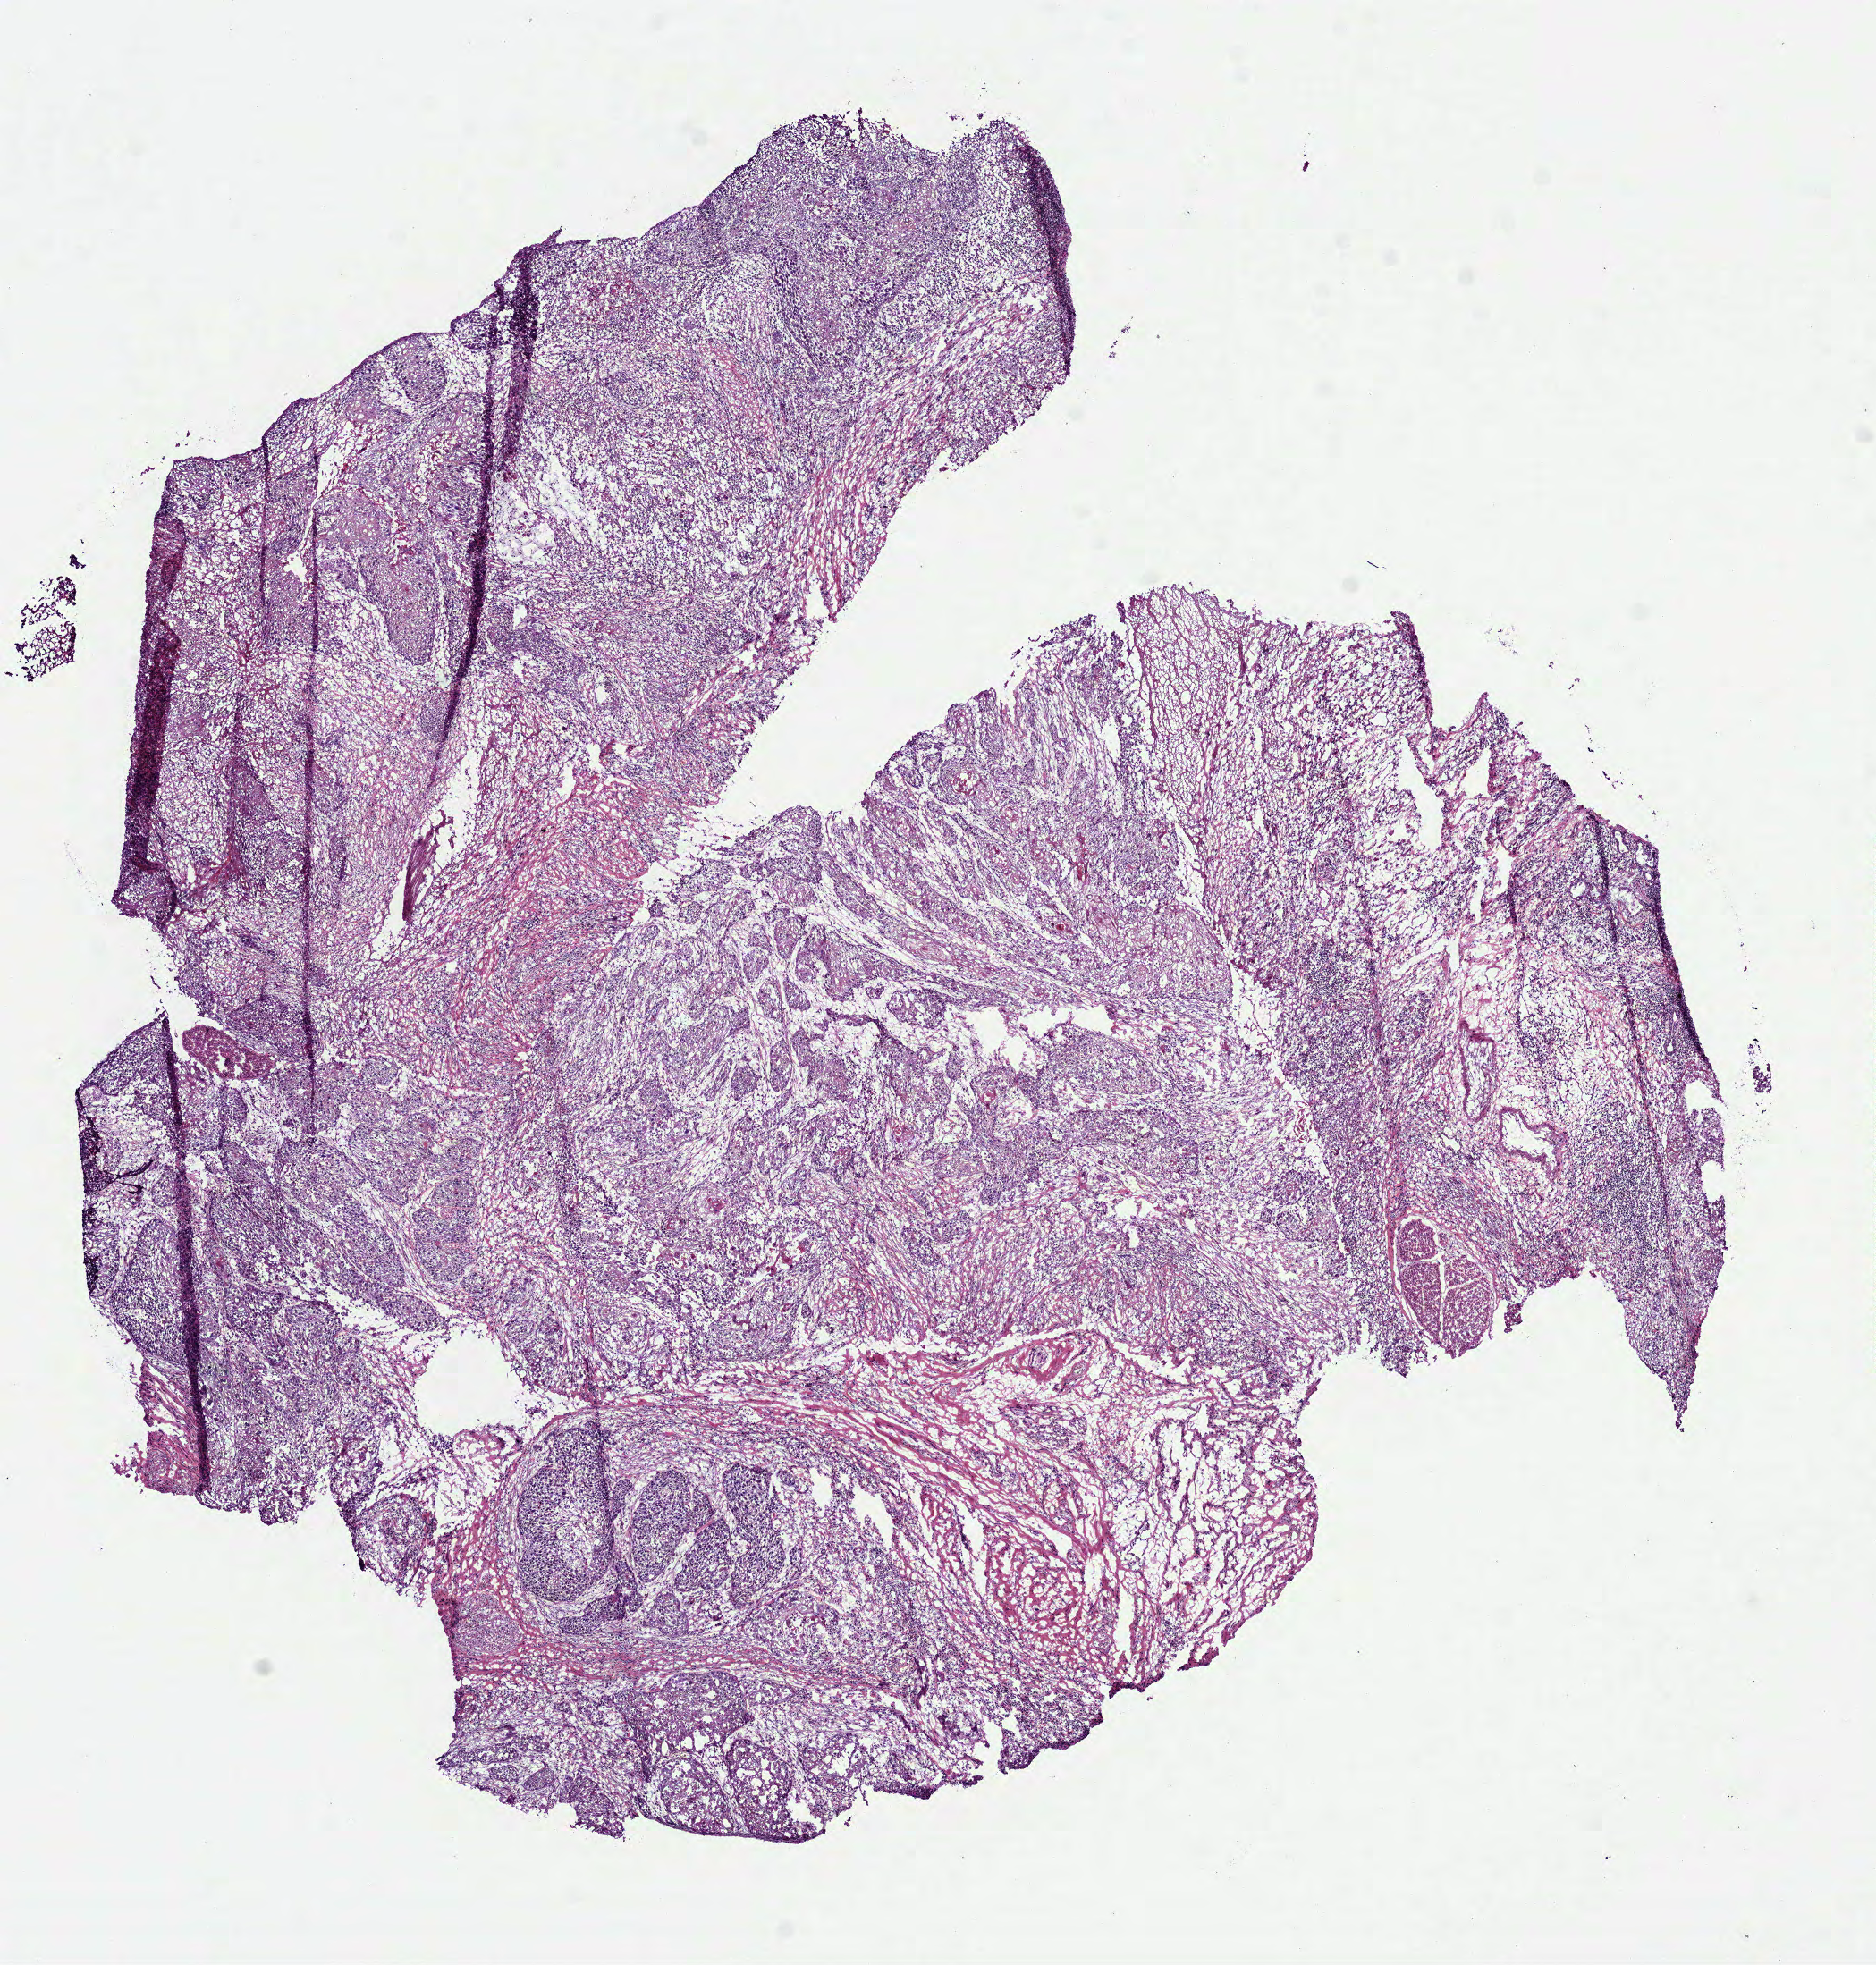
Digitized H&E-stained tissue section (whole slide) — a low-resolution overview of the entire scanned area, about 8.5 x 8.9 mm (slide scanned at 40x). Frozen section from the bottom of the tissue portion. Sample: primary tumour, head and neck. Patient: male, age at initial diagnosis 58 years. Histologic grade: G2 (moderately differentiated). Slide review estimates, as recorded: tumour cells 67%, tumour nuclei 70%, normal cells 5%, stromal cells 20%, necrosis 8%.
* AJCC pathologic stage: III (7th edition)
* TNM: T2 N1
* pathologic diagnosis: Squamous cell carcinoma, NOS (floor of mouth, NOS)